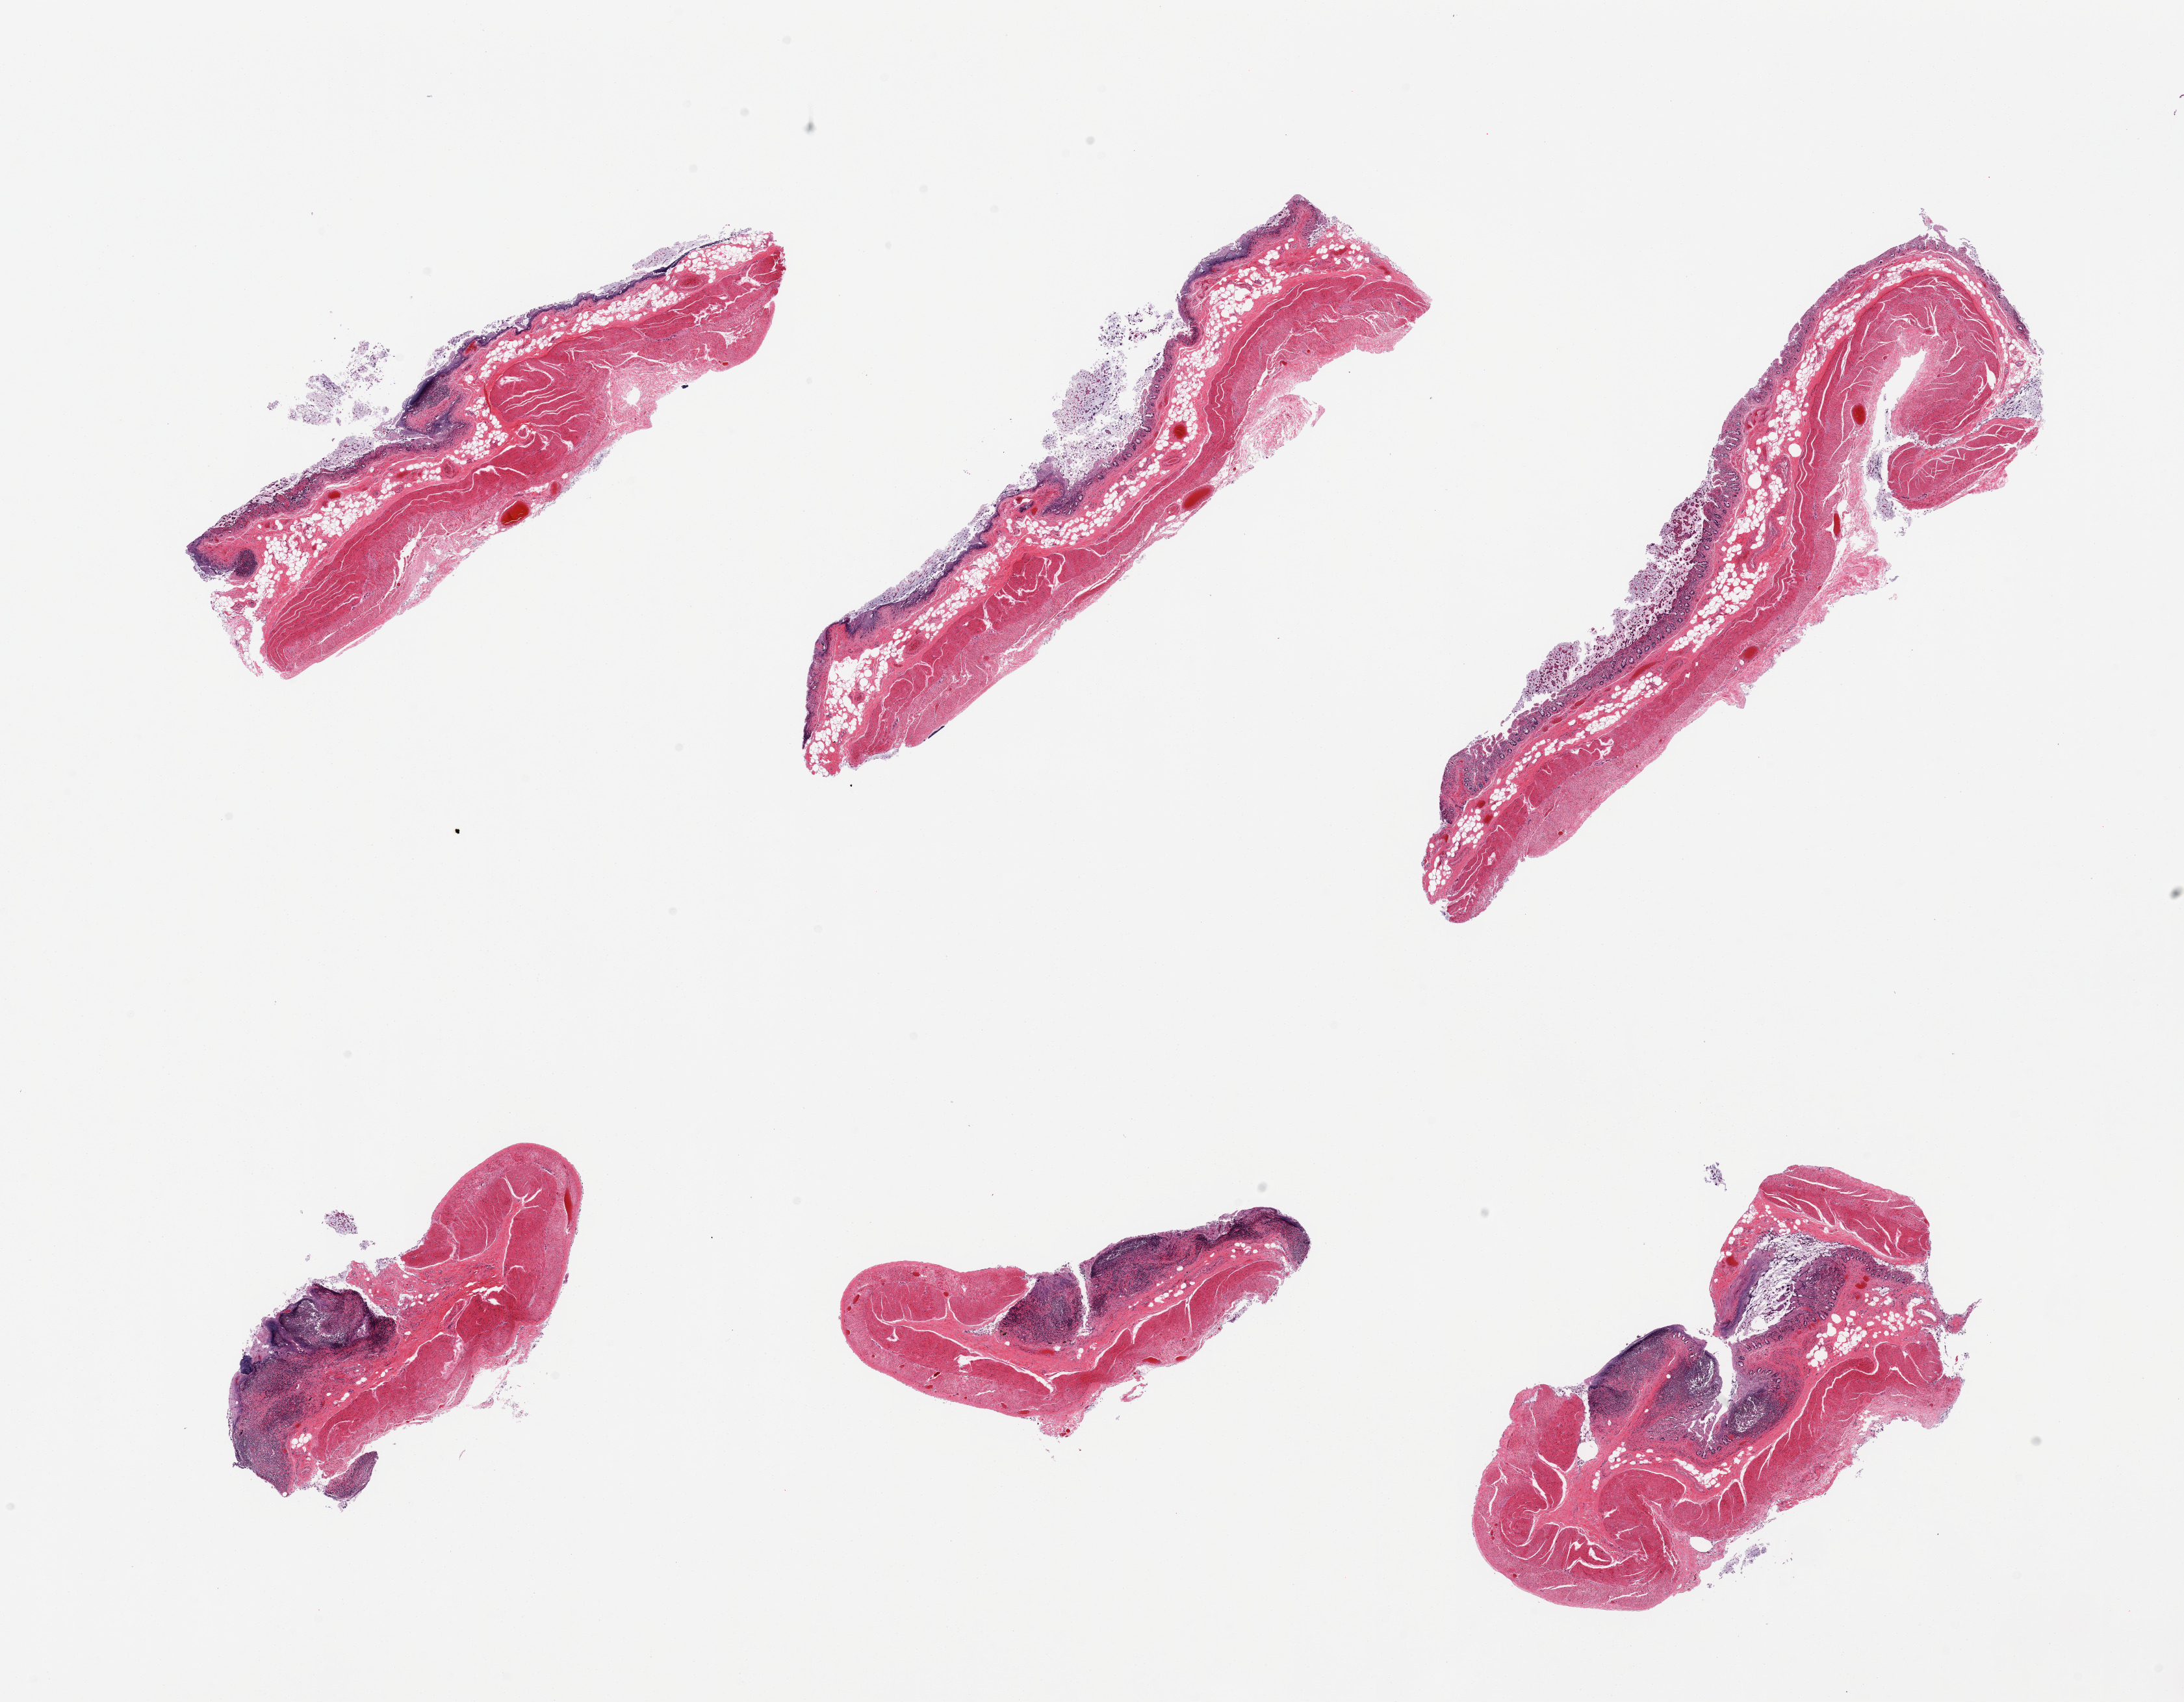
Whole-slide image, haematoxylin and eosin stain, whole scanned area (about 26.6 x 20.7 mm) shown as a low-resolution overview. PAXgene-fixed paraffin-embedded (PFPE) section. Section of ileum (target tissue). Donor tissue sample. Donor sex: male.
Reviewer comment on this tissue sample: 6 pieces, muscularis (not target) and severely autolyzed mucosa, some pieces with good lymphoid component.